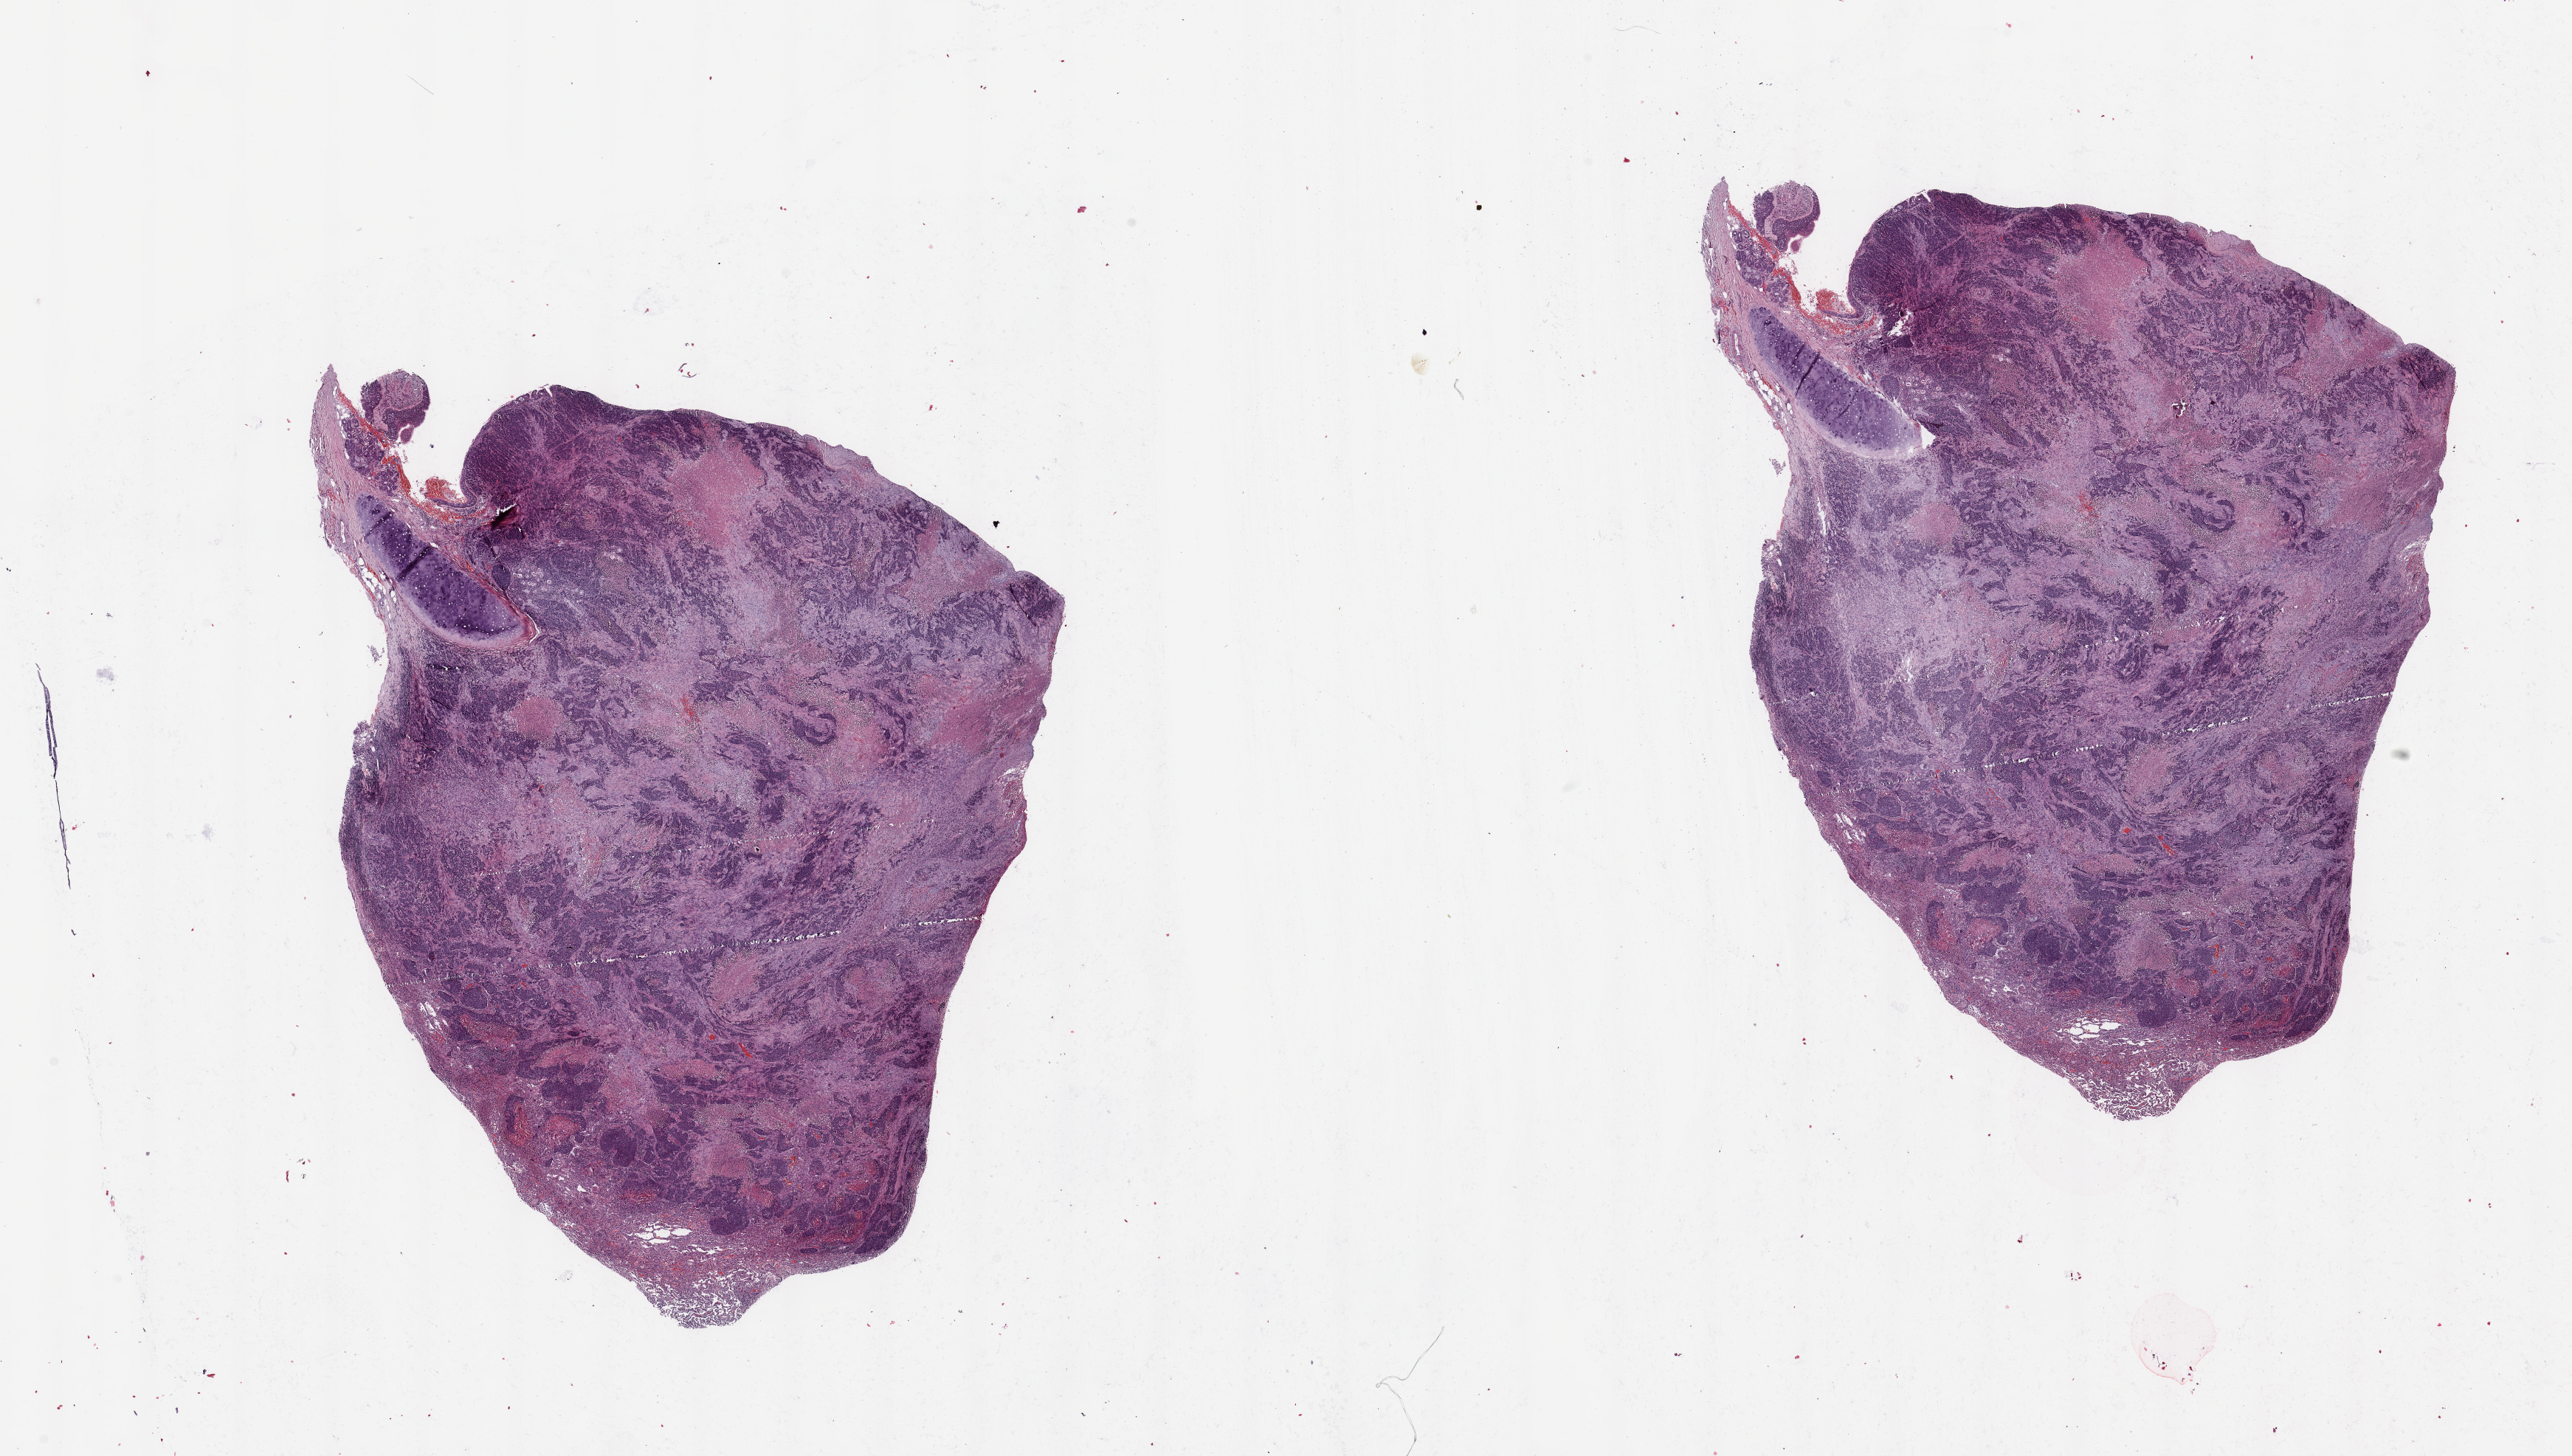
Digitized Hematoxylin and eosin (H&E) stained tissue section (whole slide) — a low-resolution overview of the entire scanned area, about 27.6 x 15.6 mm, tumour tissue sample, sampled site: lung. Patient: male, age 54 years. Histologic grade: G2 (moderately differentiated). Composition of this section per pathologist review: tumour nuclei 50%, necrosis 20%.
• diagnosis: Squamous cell carcinoma, NOS
• AJCC pathologic stage: IIIA